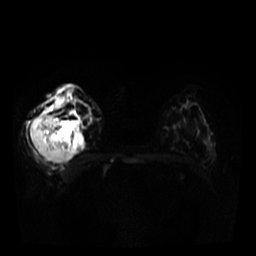
Breast MRI, one axial slice. Position 19 of 34 along the scan axis. Diffusion-weighted series; image 2 of 4 stored at this slice position (different b-values; order by instance number). 3 T. 5 mm slice thickness. 256 × 256 image matrix. Female patient.
Annotated regions visible in this slice (manually delineated by an expert):
- tumour on diffusion-weighted imaging: bounding box [x1, y1, x2, y2] px = [30, 117, 73, 164]